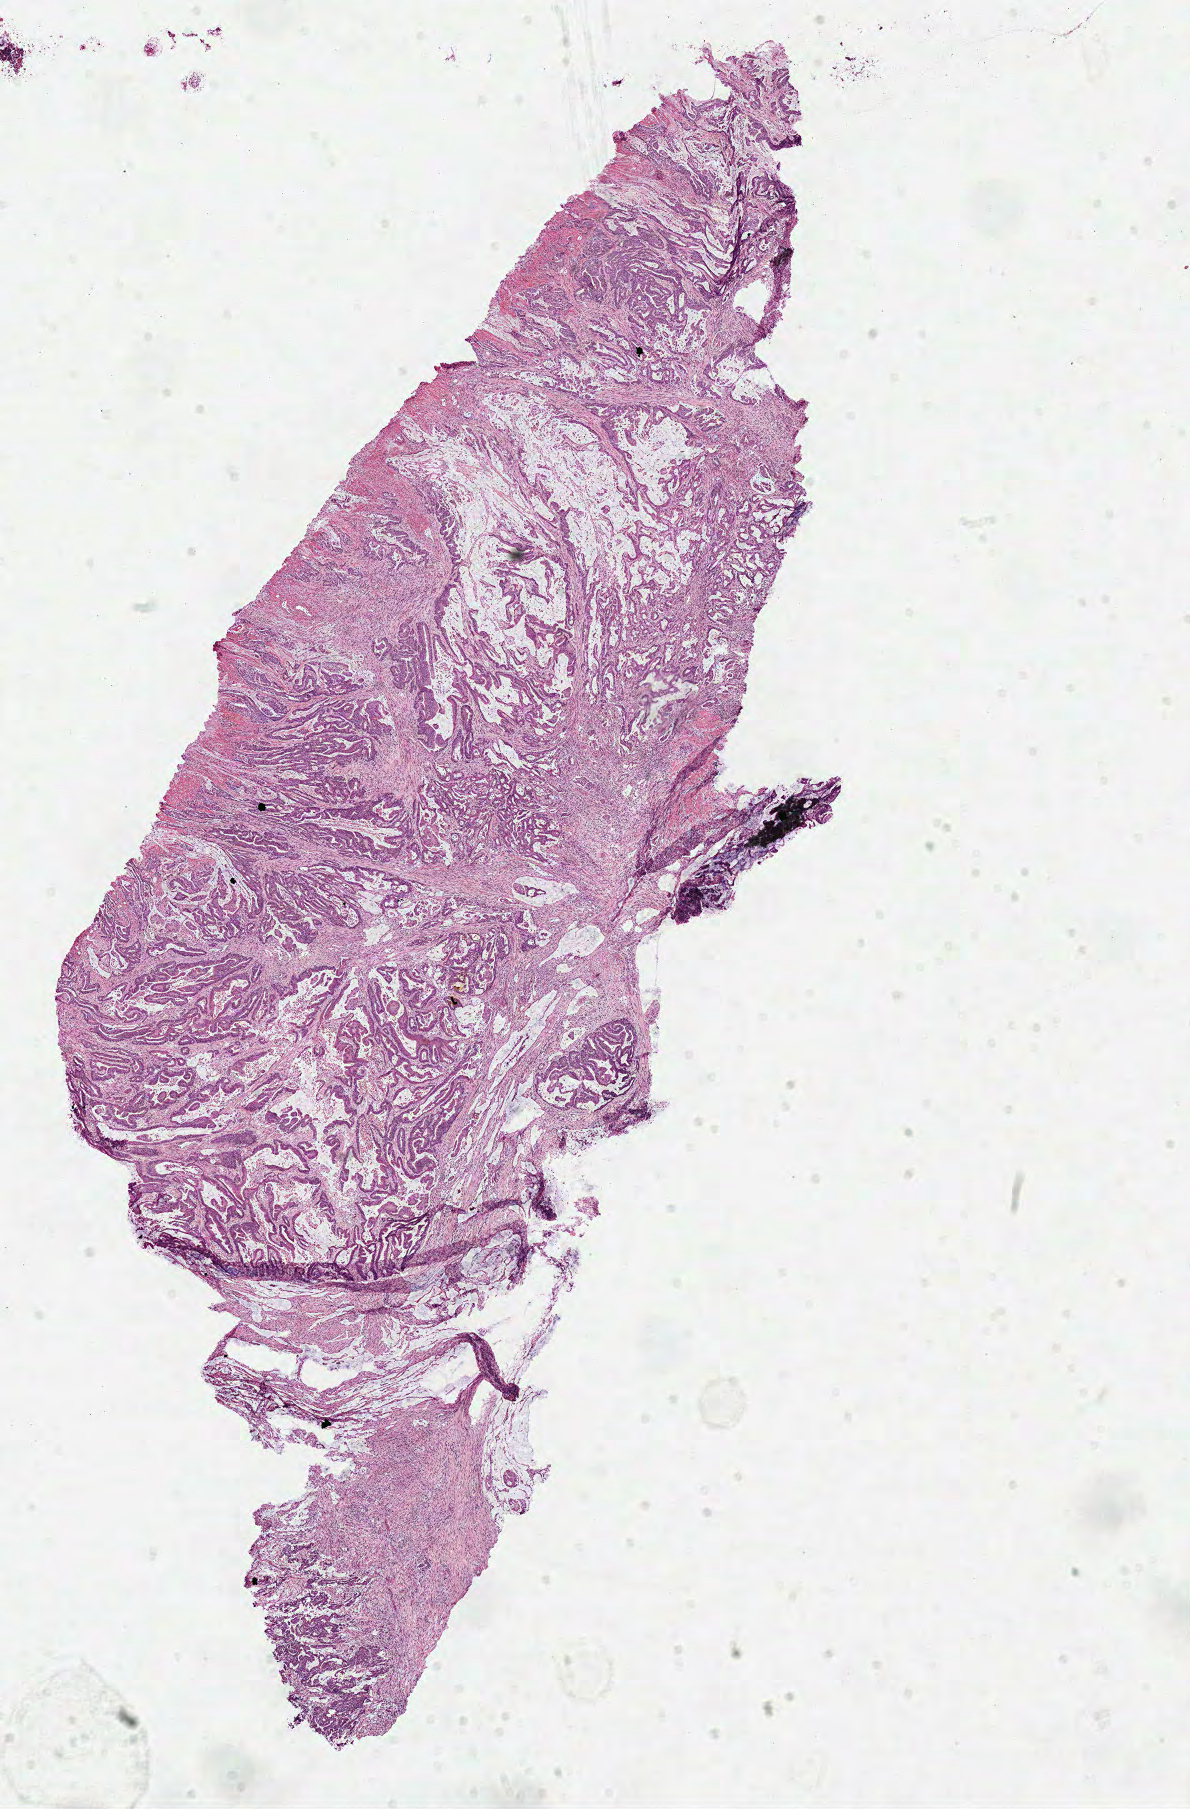
Digitized H&E-stained tissue section (whole slide), low-resolution overview of the scanned area, about 9.4 x 14.3 mm (acquisition: 40x scan); frozen section; primary tumour sample from the colon. Female, age 58 years at initial diagnosis. Slide review estimates, as recorded: tumour cells 80%, tumour nuclei 80%, normal cells 0%, stromal cells 20%, necrosis 0%.
TNM: T3 N0 M0. Histologic diagnosis: Adenocarcinoma, NOS (cecum). AJCC pathologic stage: IIA. Lymph nodes positive (case pathology): 0 of 15 examined.